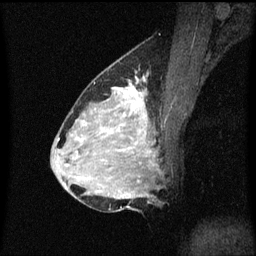
Breast MRI (dynamic contrast-enhanced), one sagittal slice. Slice 31 of 60 in the series (ordered by position). Dynamic contrast-enhanced series, image 2 of 3 at this slice position (ordered by acquisition). 1.5 T. TE 4.2 ms, TR 8.4 ms. 2 mm slice thickness. 256 × 256 image matrix, field of view 200 × 200 mm. Patient: female, 34 years. Case-level facts recorded for this patient, not image findings: setting: breast cancer imaged before/during neoadjuvant chemotherapy; receptor status: HR-positive, HER2-negative.
Structures marked on this image (semi-automatic segmentation, software-assisted and operator-edited):
- analysis volume of interest (the breast-tissue region the enhancement analysis was run in; not a lesion): bounding box (x1, y1, x2, y2) in pixels: (69, 70, 163, 209)
- tumour enhancement mask (voxels above the 70 % enhancement threshold inside the analysis volume of interest): (101, 88, 150, 183)